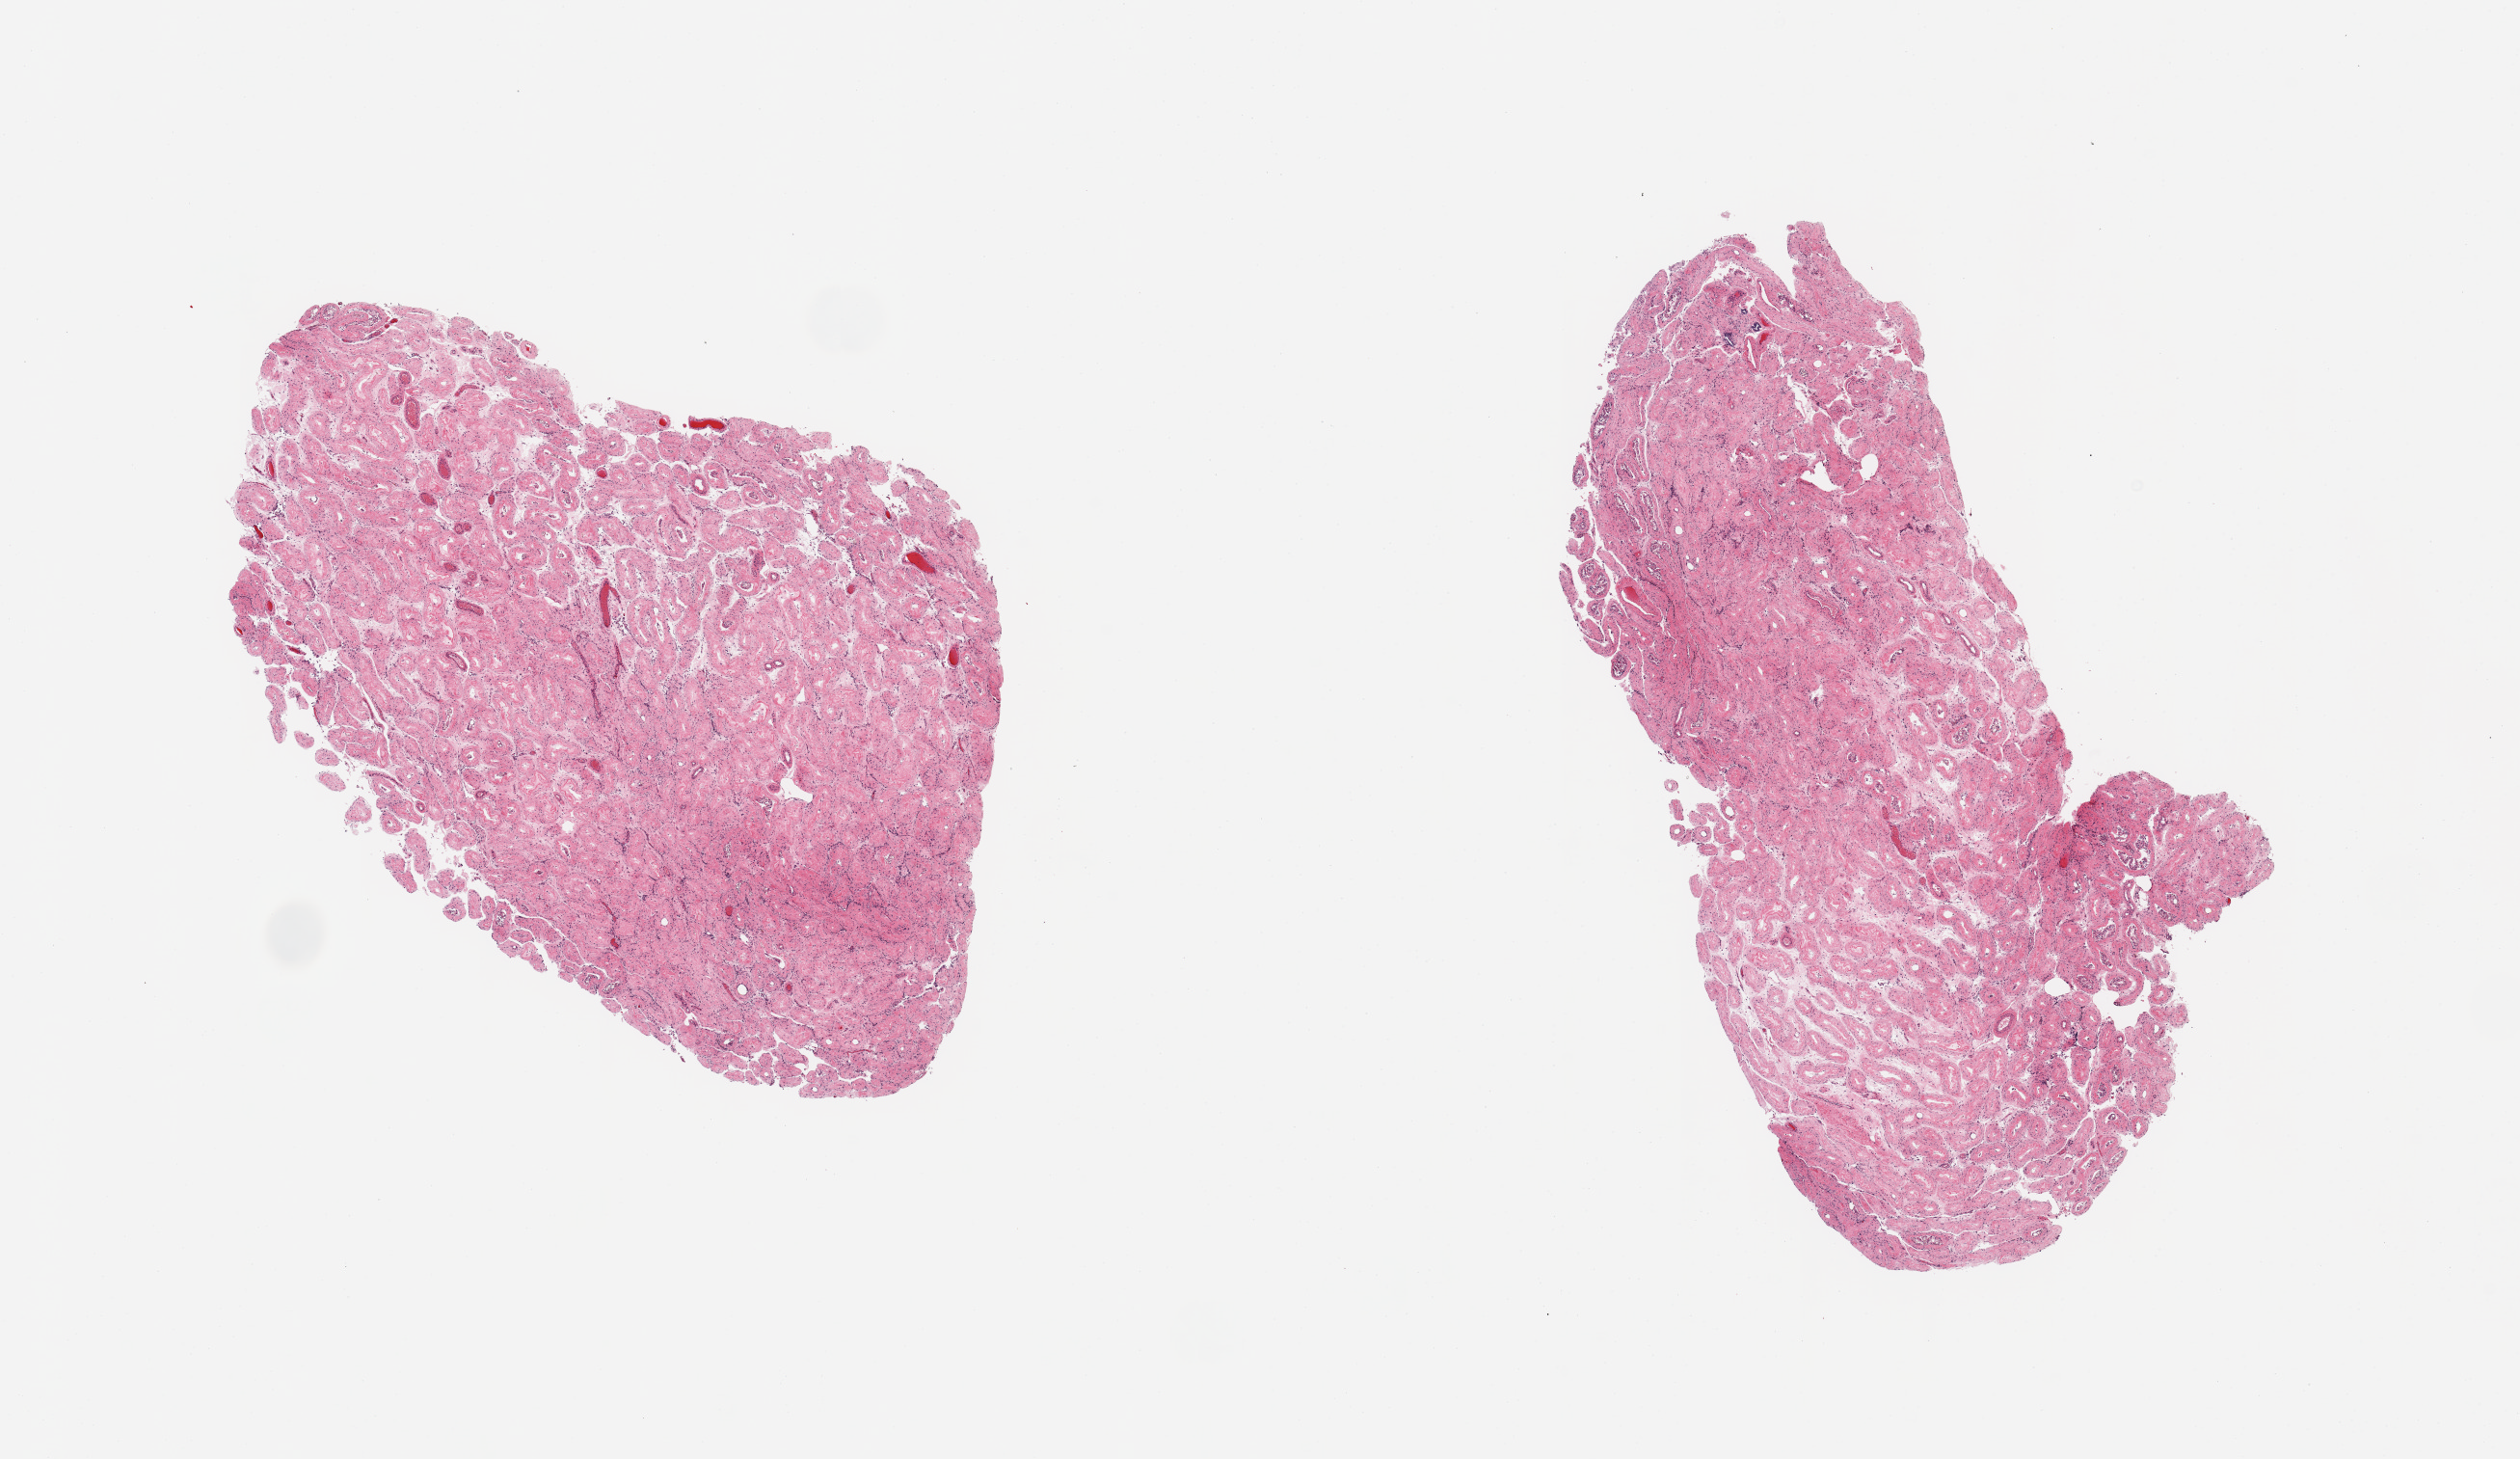
Hematoxylin and eosin (H&E) whole-slide image — whole scanned area (about 20.7 x 12.0 mm) shown as a low-resolution overview. PAXgene-fixed, paraffin-embedded tissue. Section of testis (target tissue). Donor tissue sample. Male donor.
* reviewer comment on this tissue sample: 2 pieces; hyalinized tubules, no spermatogenesis